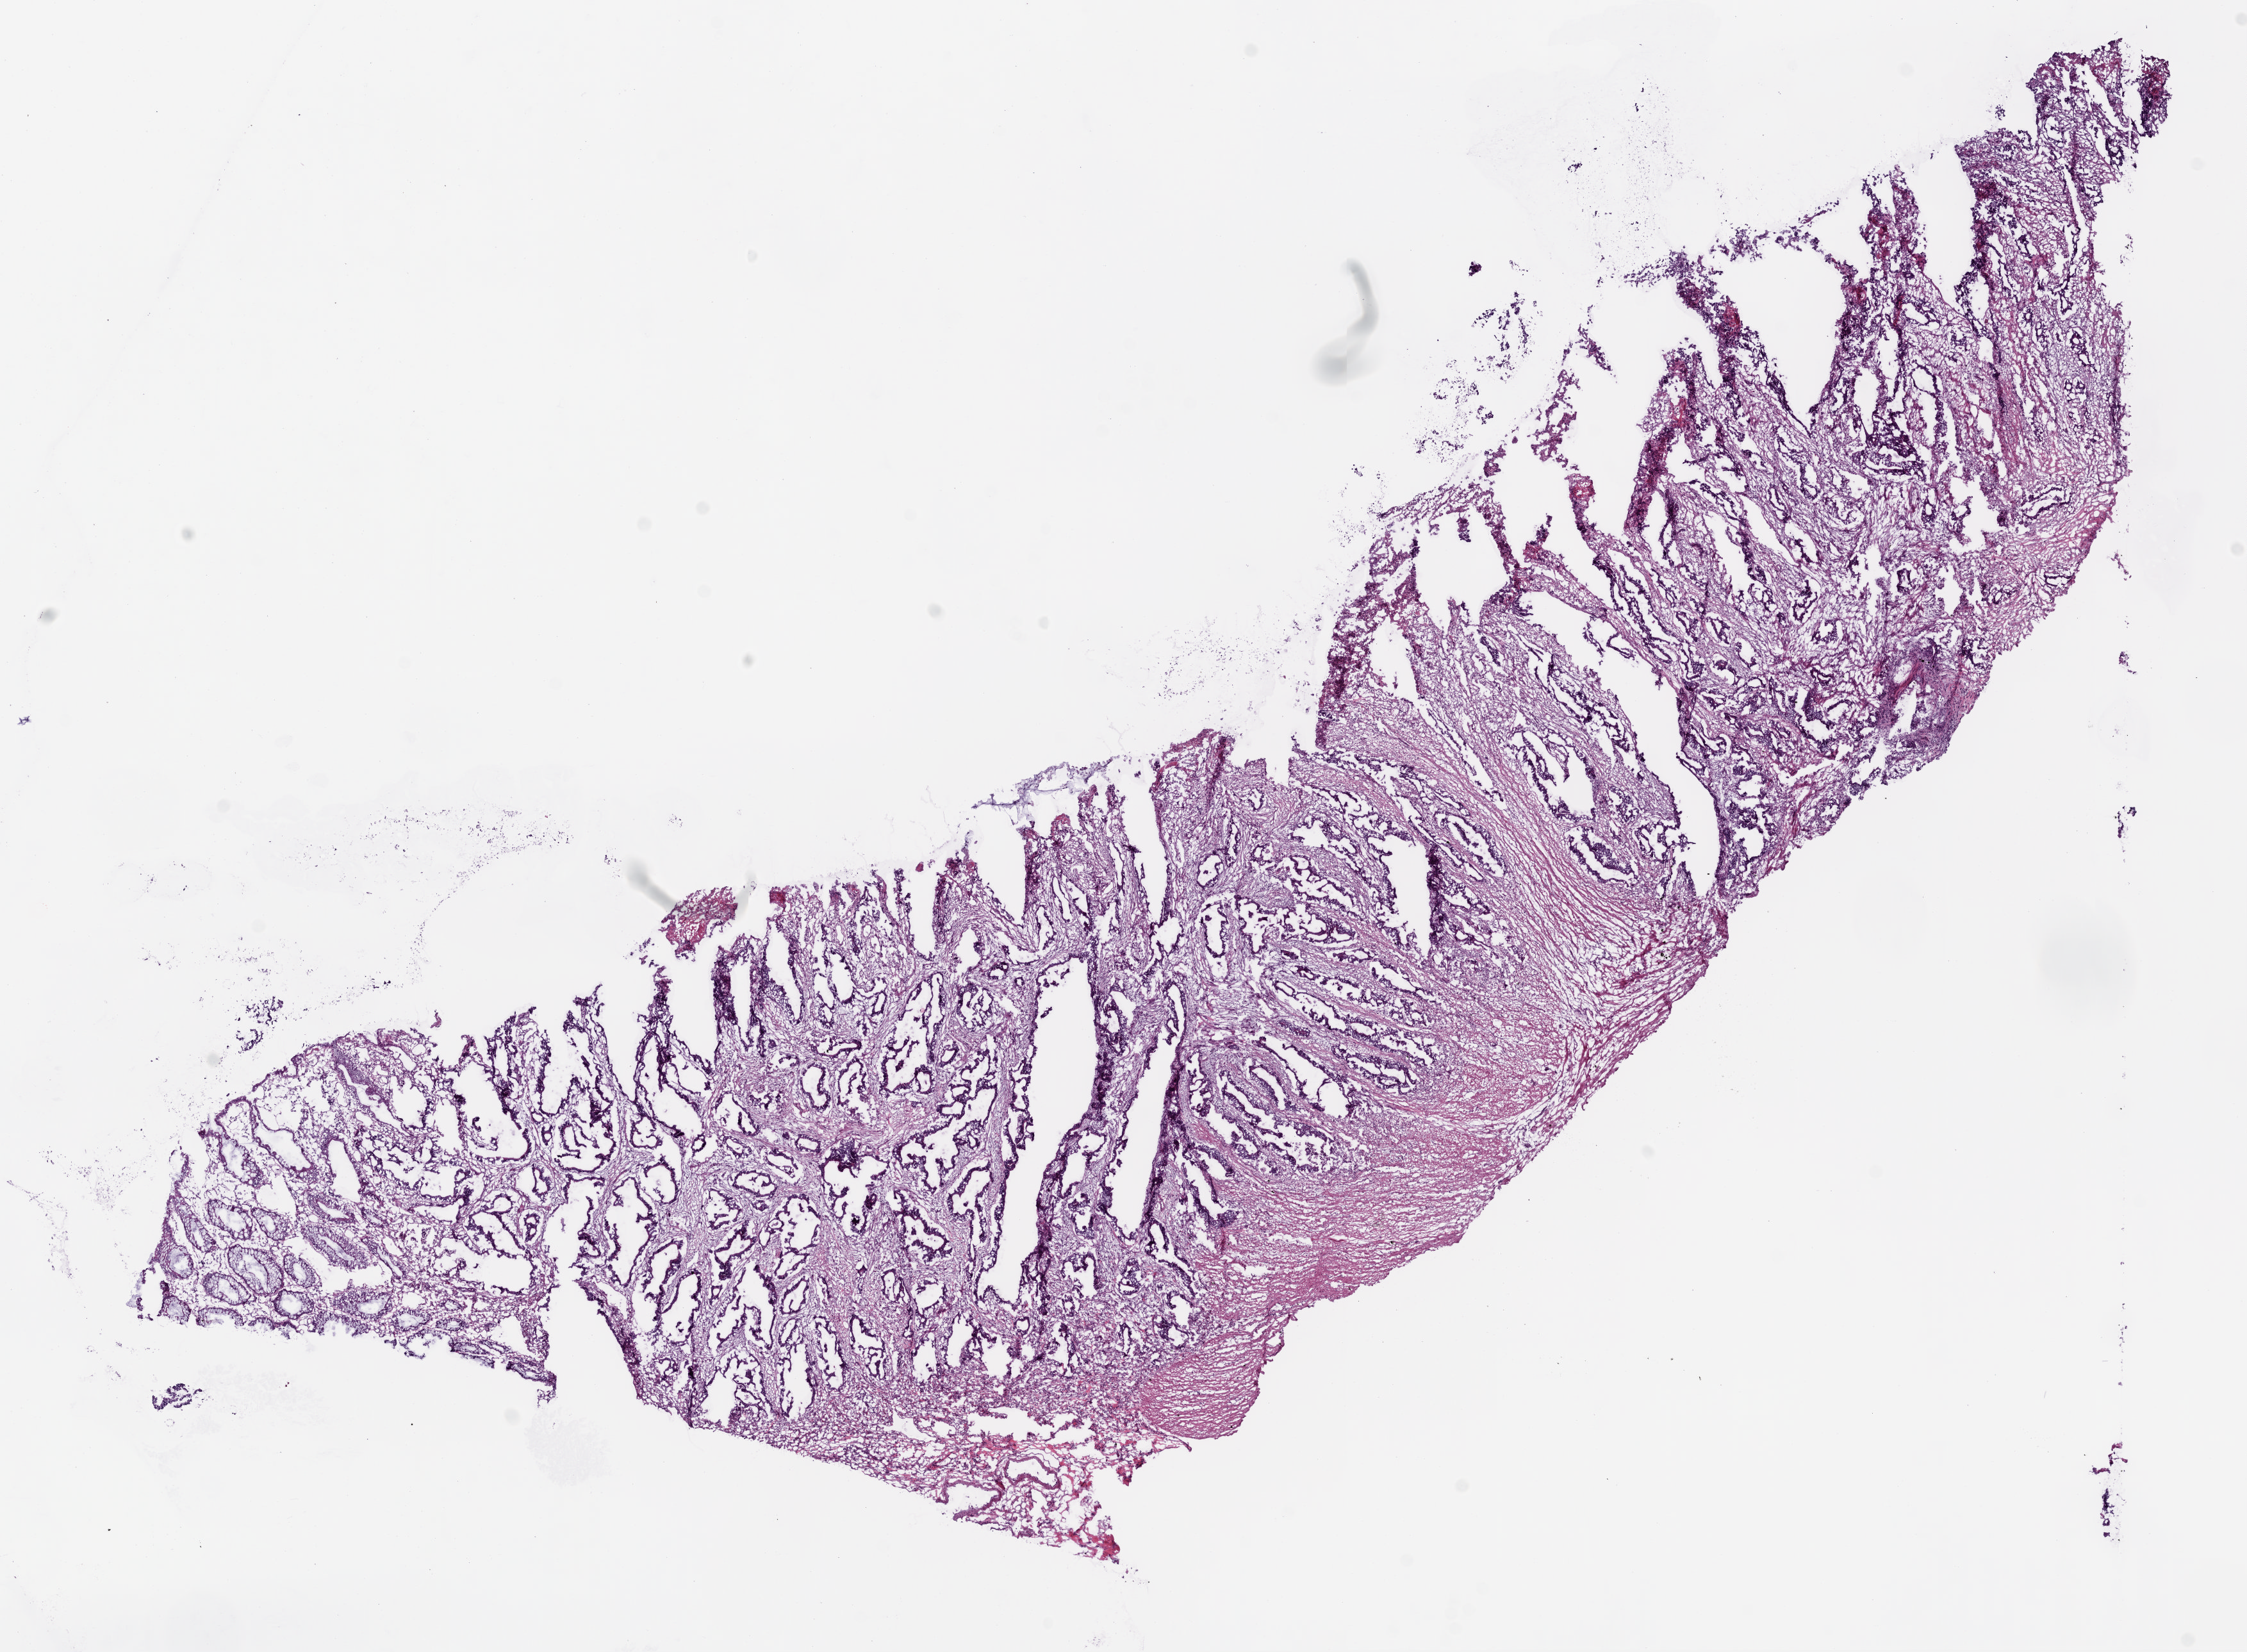
Whole-slide histology image, H&E — whole scanned area (about 14.1 x 10.3 mm, slide scanned at 5x) shown as a low-resolution overview; frozen section; colon, primary tumour sample. Patient: male, age at initial diagnosis 43 years. Pathologist review of this section (percent, as recorded): tumour cells 65%, tumour nuclei 75%, normal cells 5%, stromal cells 30%, necrosis 0%.
Histologic diagnosis: Adenocarcinoma, NOS (descending colon). TNM: T3 N0 MX. Lymph nodes positive (case pathology): 0 of 12 examined. AJCC pathologic stage: II (5th edition).